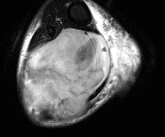
MRI of an extremity soft-tissue mass, one axial slice; position 37 of 81 along the scan axis; T2-weighted fat-saturated; MR volume resampled by the dataset authors to the PET/CT grid (not the native acquisition matrix); 165 × 137 image matrix, field of view 161 × 134 mm. Male patient. Case-level facts recorded for this patient, not image findings: histological type: liposarcoma - round cell; grade: high; site of the primary tumour: right calf.
Outlined on this slice (expert contour drawn on MRI and transferred to this co-registered scan by the dataset authors):
- gross tumour volume (mass): bounding box <23,27,136,119> (left, top, right, bottom; pixels)